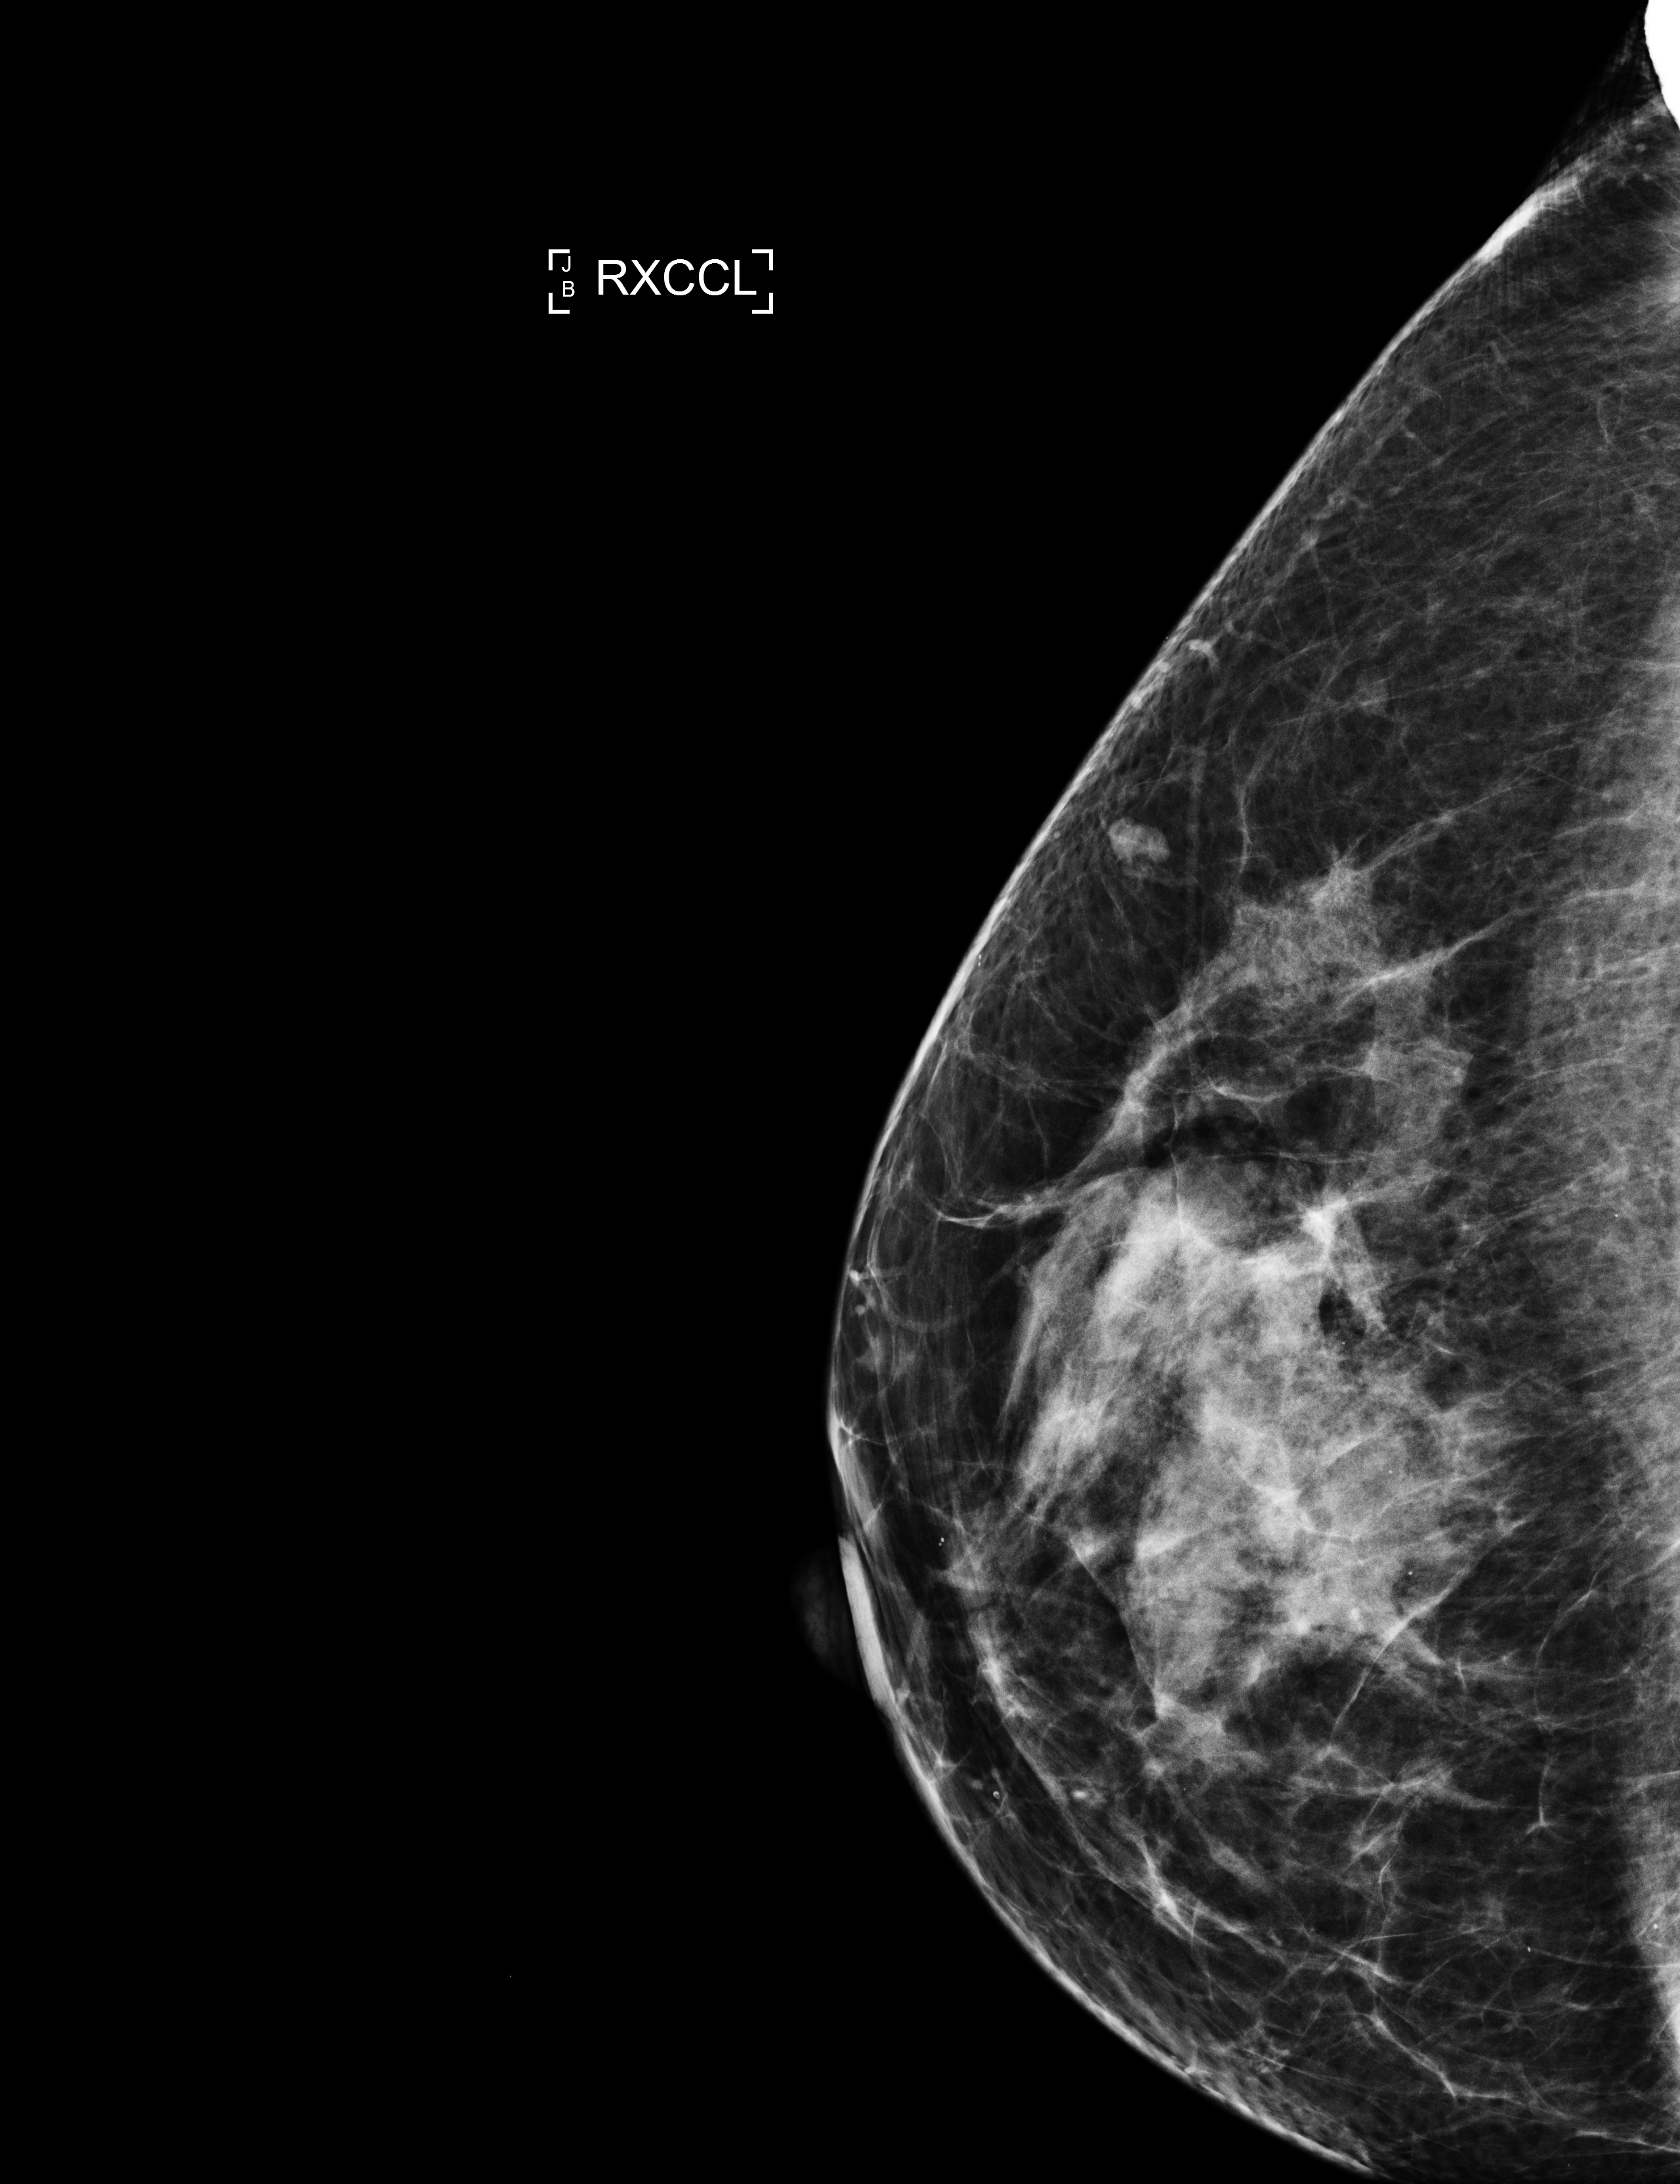
Annual screening mammography examination; compressed breast thickness 60 mm; system: Selenia Dimensions. Female patient, age 61 years.
Image type: full-field digital mammogram. Breast: right. Projection: laterally exaggerated craniocaudal (XCCL) view.